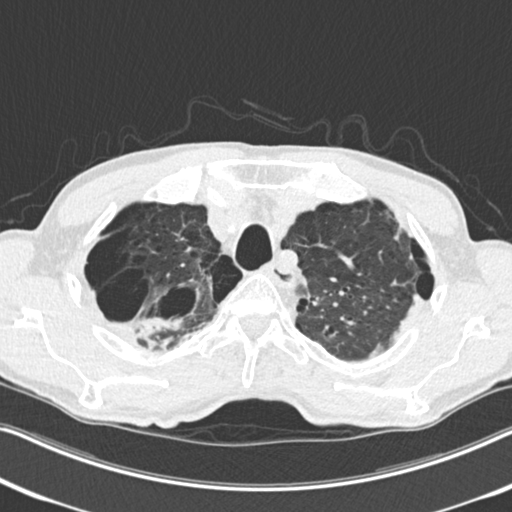
Low-dose screening chest CT, one axial slice. Position 209 of 251 along the scan axis. 120 kVp. Lung window (W 1500 / L -600 HU). 2 mm slice thickness. 512 × 512 image matrix, field of view 334 × 334 mm.
Outlined on this slice (manually delineated by an expert):
- lesion 1 (tumor, upper lobe of right lung): bounding box [x1, y1, x2, y2] px = [127, 317, 182, 337]